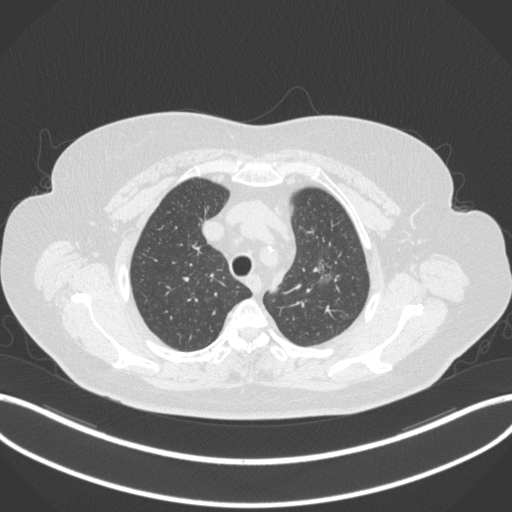
Chest CT, one axial slice. Position 269 of 310 along the scan axis. Reconstruction kernel B31f. Lung window (W 1500 / L -600 HU). 512 × 512 image matrix, field of view 400 × 400 mm. Patient: female, 70 years. From the clinical record (not read from this slice): clinical TNM (as recorded): T1c N0 M0.
Annotated regions visible in this slice (rectangle marked by the reading radiologist):
- lung tumour (recorded histology: adenocarcinoma): bounding box [x1, y1, x2, y2] px = [310, 255, 340, 290]